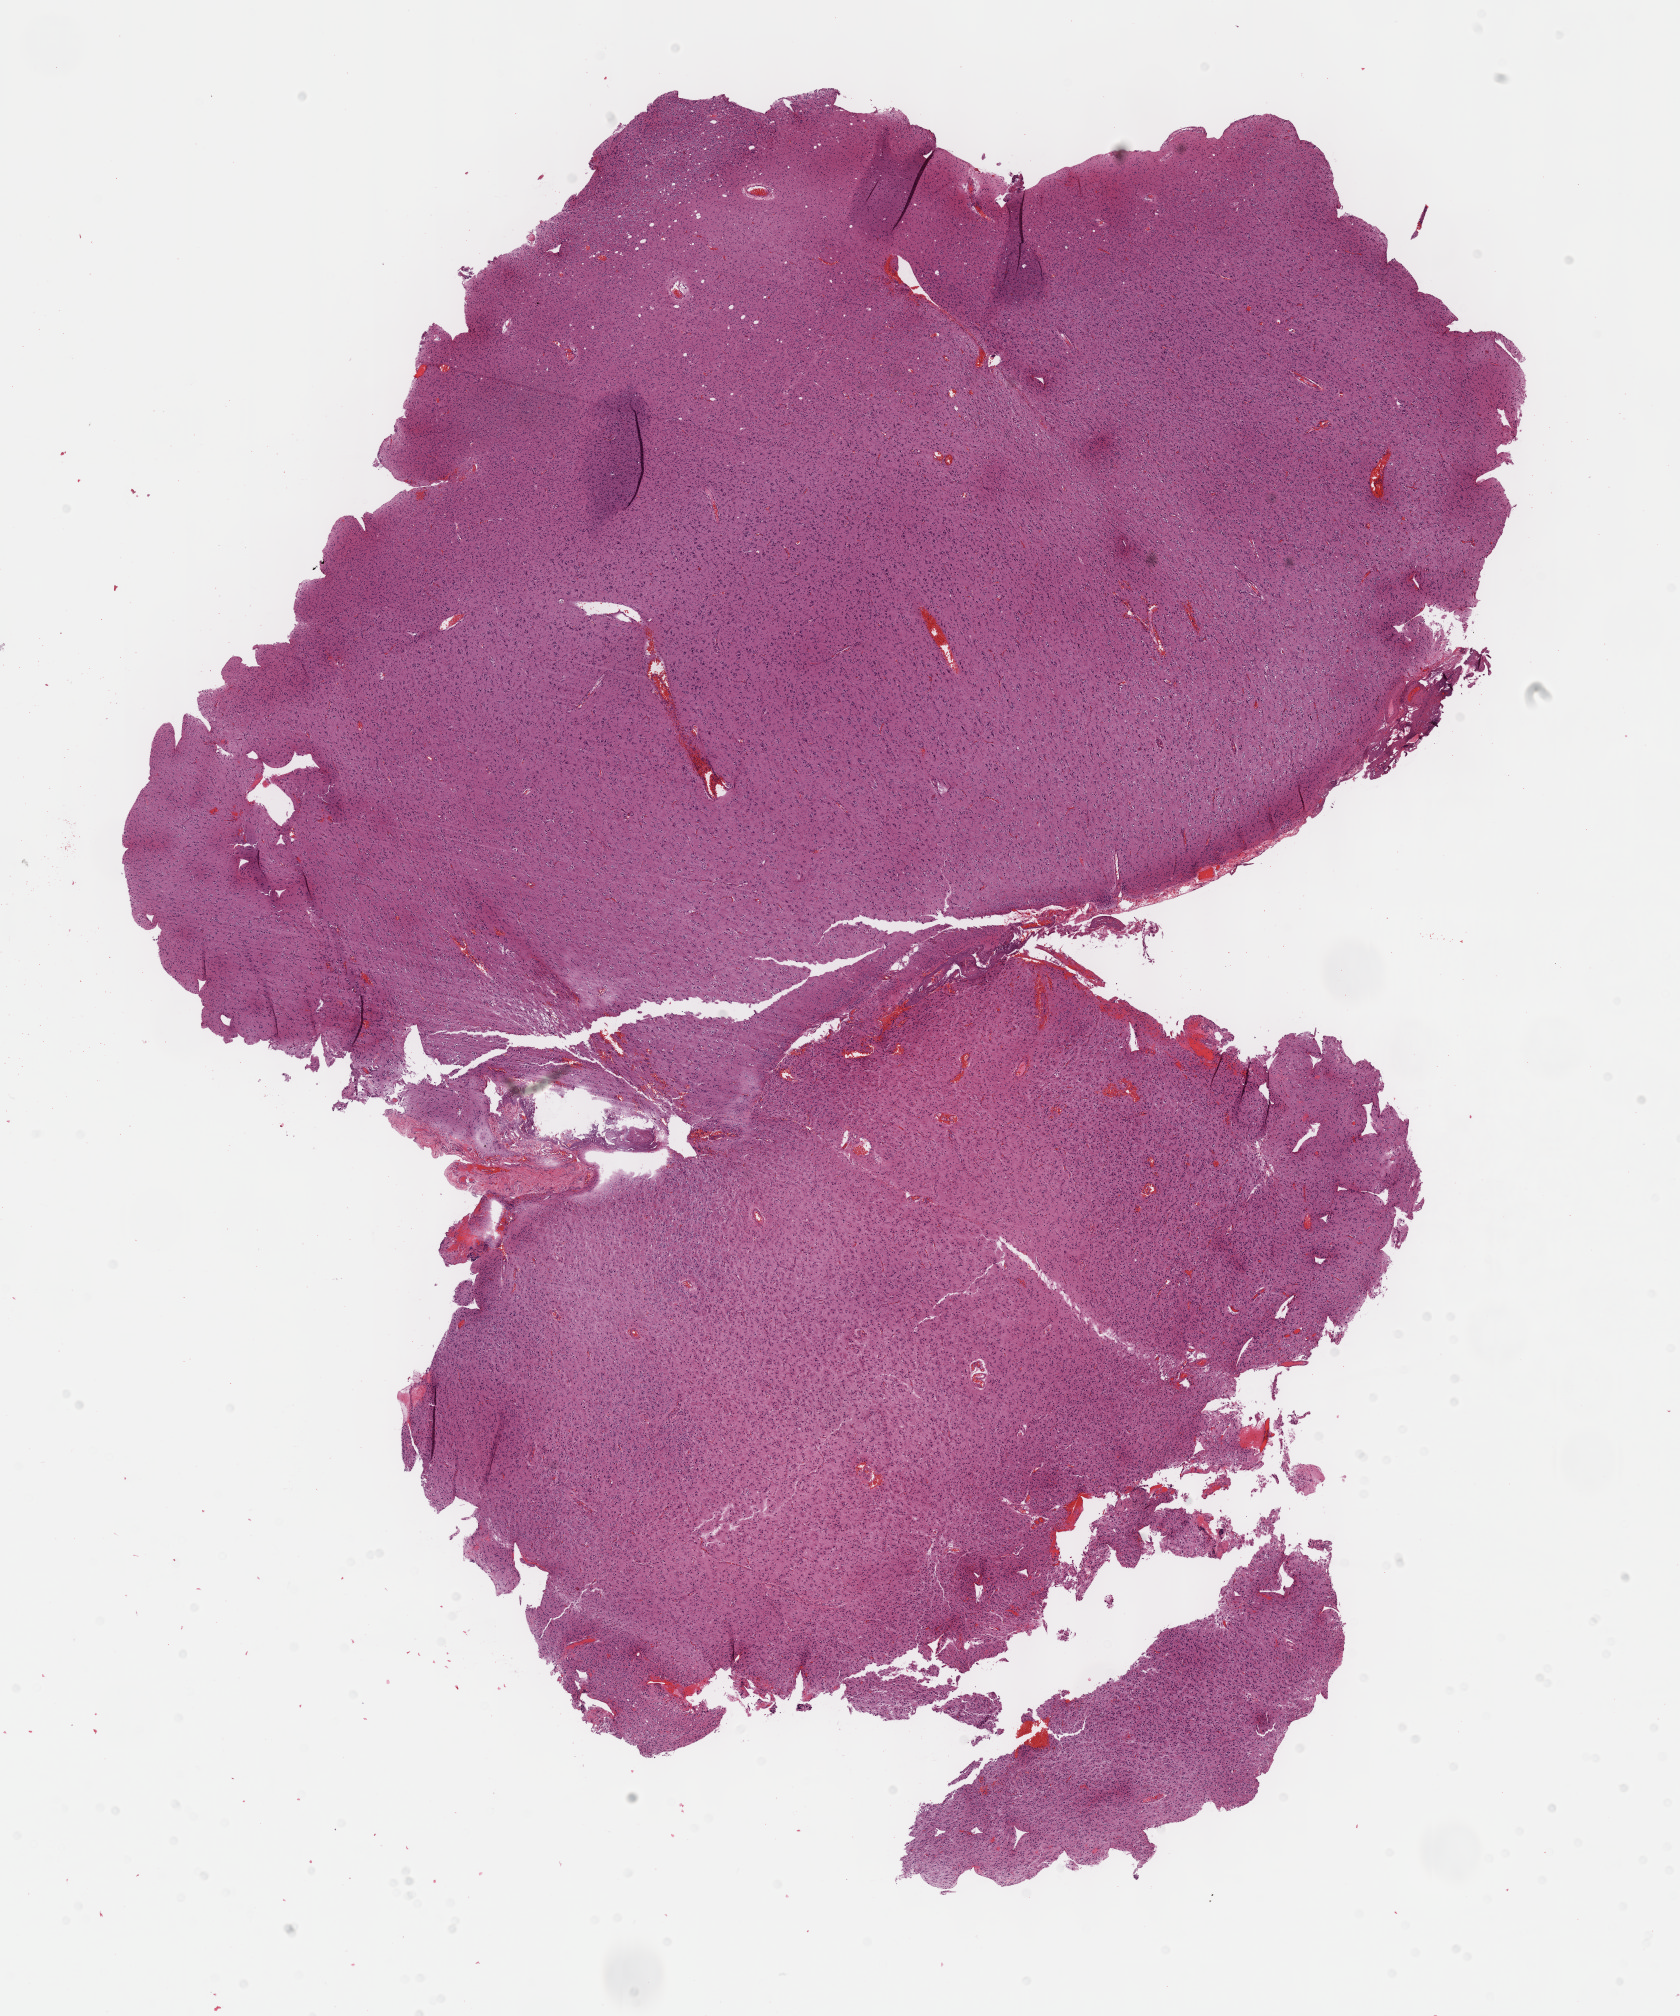
Whole-slide histology image, H&E — shown as a low-resolution overview of the whole scanned area (about 13.6 x 16.3 mm, slide scanned at 40x); formalin-fixed paraffin-embedded (FFPE) diagnostic section; primary tumour sample from the brain. Patient: male, age at initial diagnosis 54 years. Histologic grade: G2 (moderately differentiated).
Diagnosis: Oligodendroglioma, NOS.